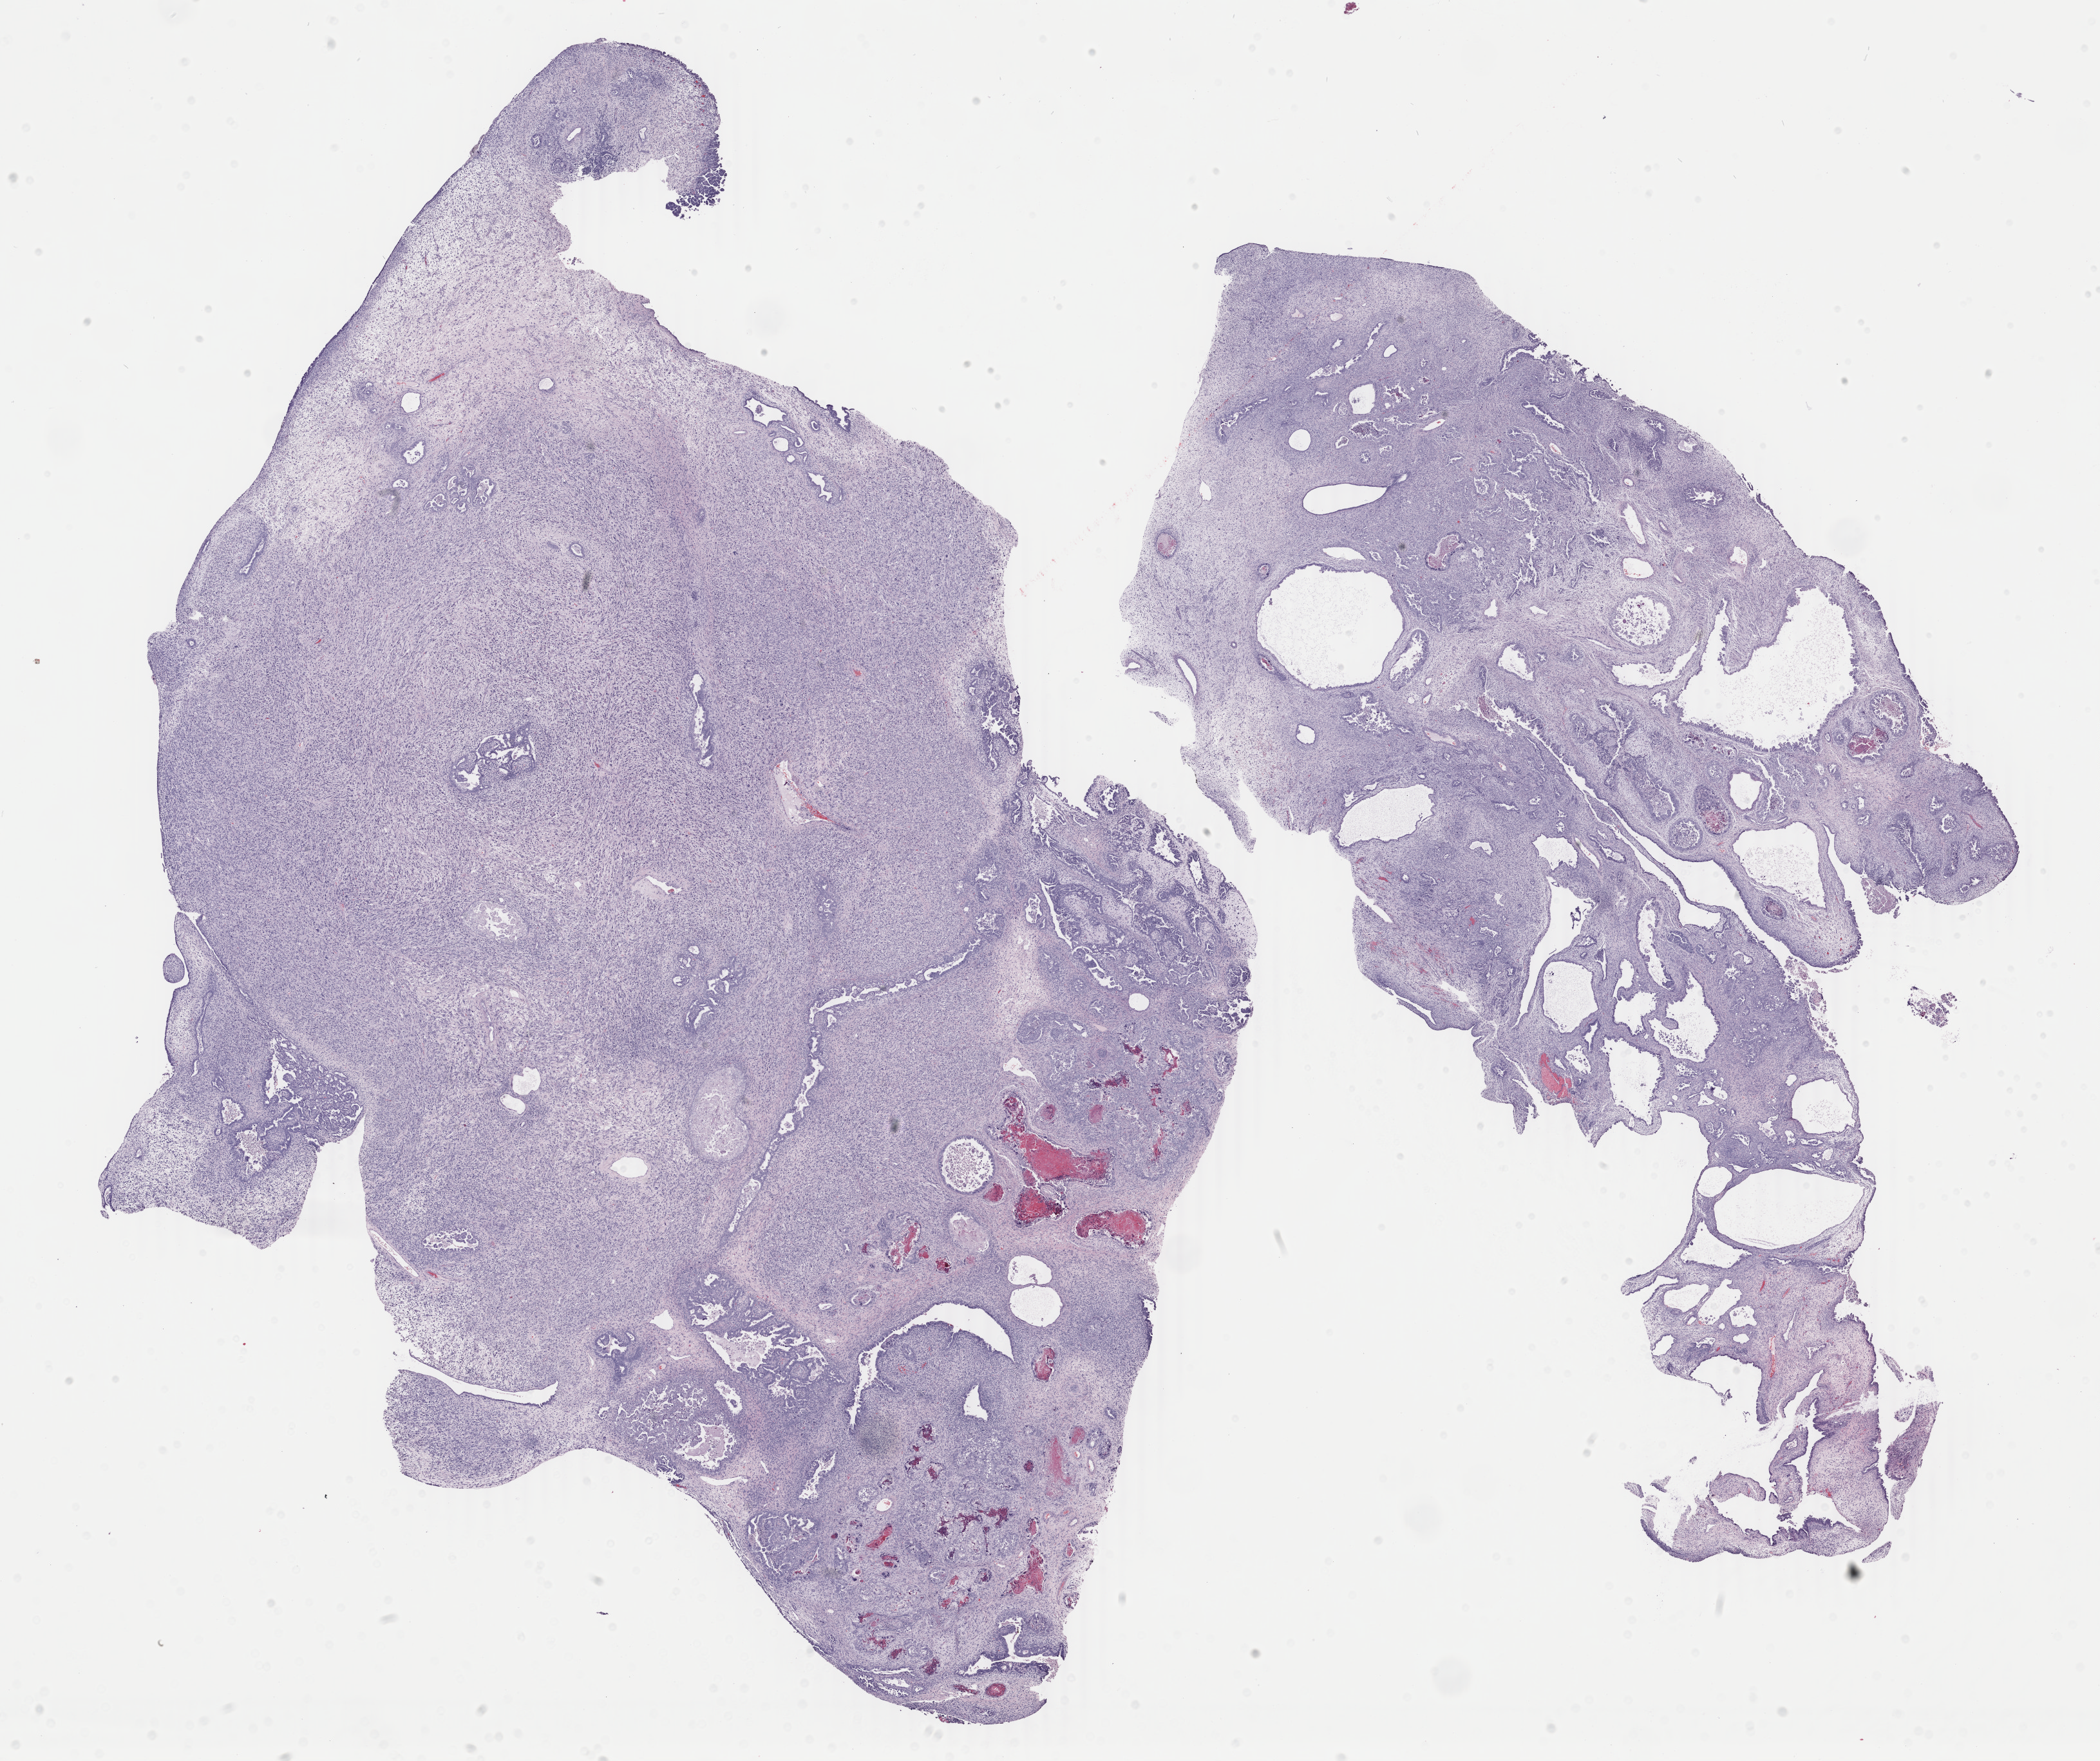
Digitized Hematoxylin and eosin (H&E) stained tissue section (whole slide) — shown as a low-resolution overview of the whole scanned area (about 25.9 x 21.8 mm, from a 40x scan), FFPE section, uterus, primary tumour sample. Female patient; age at initial diagnosis 61 years.
* diagnosis: Mullerian mixed tumor (endometrium)
* lymph nodes positive (case pathology): 3 of 3 examined
* FIGO stage: IVB